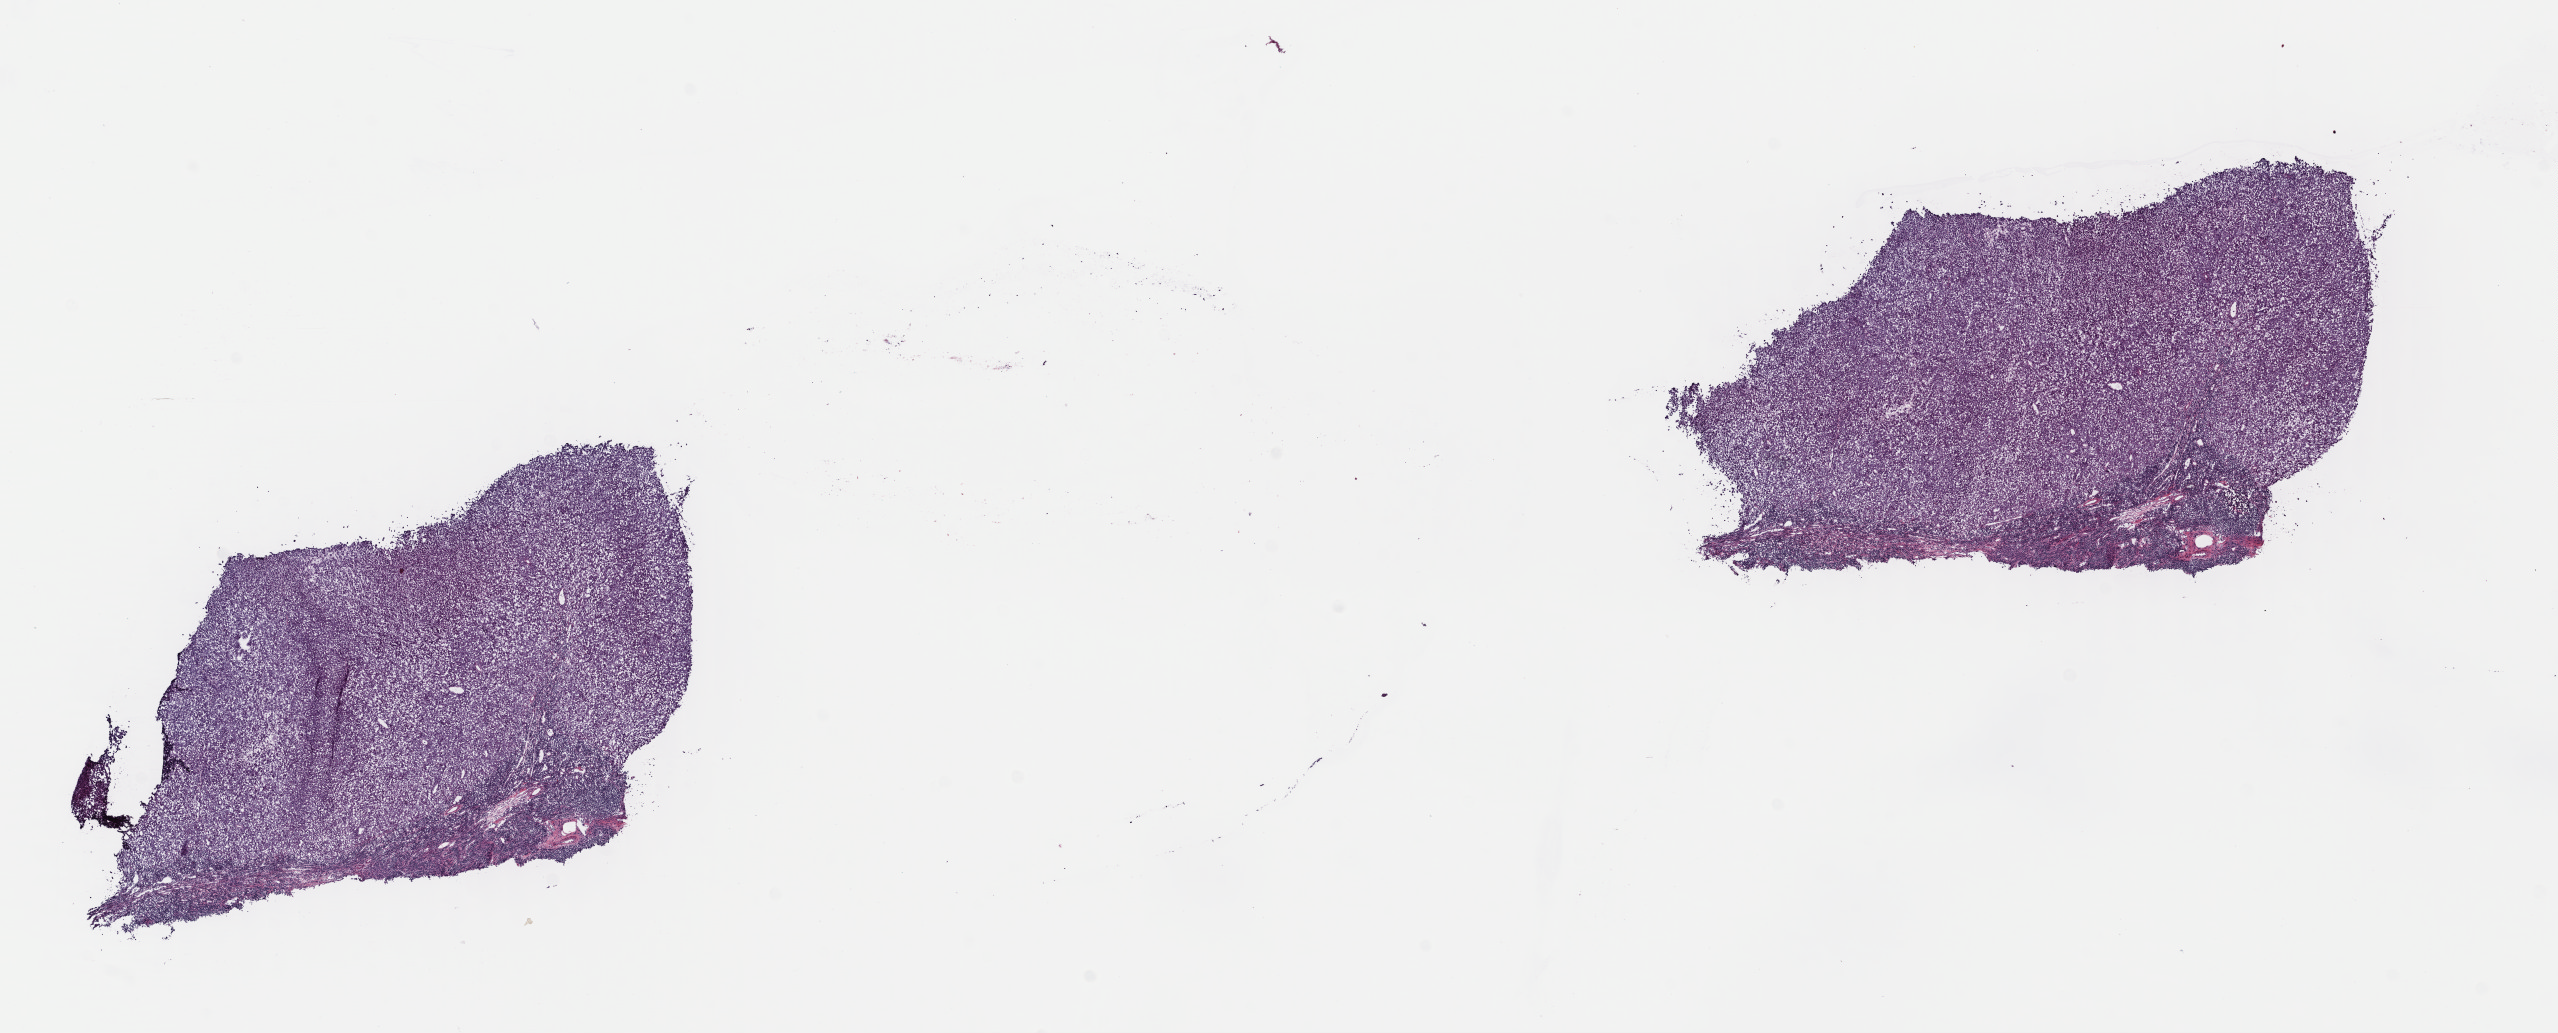
Digitized H&E tissue section (whole slide) — low-resolution overview of the scanned area, about 20.1 x 8.1 mm (from a 40x scan); frozen section from the top of the tissue portion; metastatic tumour sample, sampled site not recorded. Male, age 73 years at initial diagnosis. Slide review estimates, as recorded: tumour cells 95%, tumour nuclei 90%, normal cells 2%, stromal cells 1%, necrosis 2%. Inflammatory infiltration, as recorded: lymphocyte infiltration 7%, monocyte infiltration 0%, neutrophil infiltration 0%.
This section: metastatic tumour tissue. Patient diagnosis: Malignant melanoma, NOS.